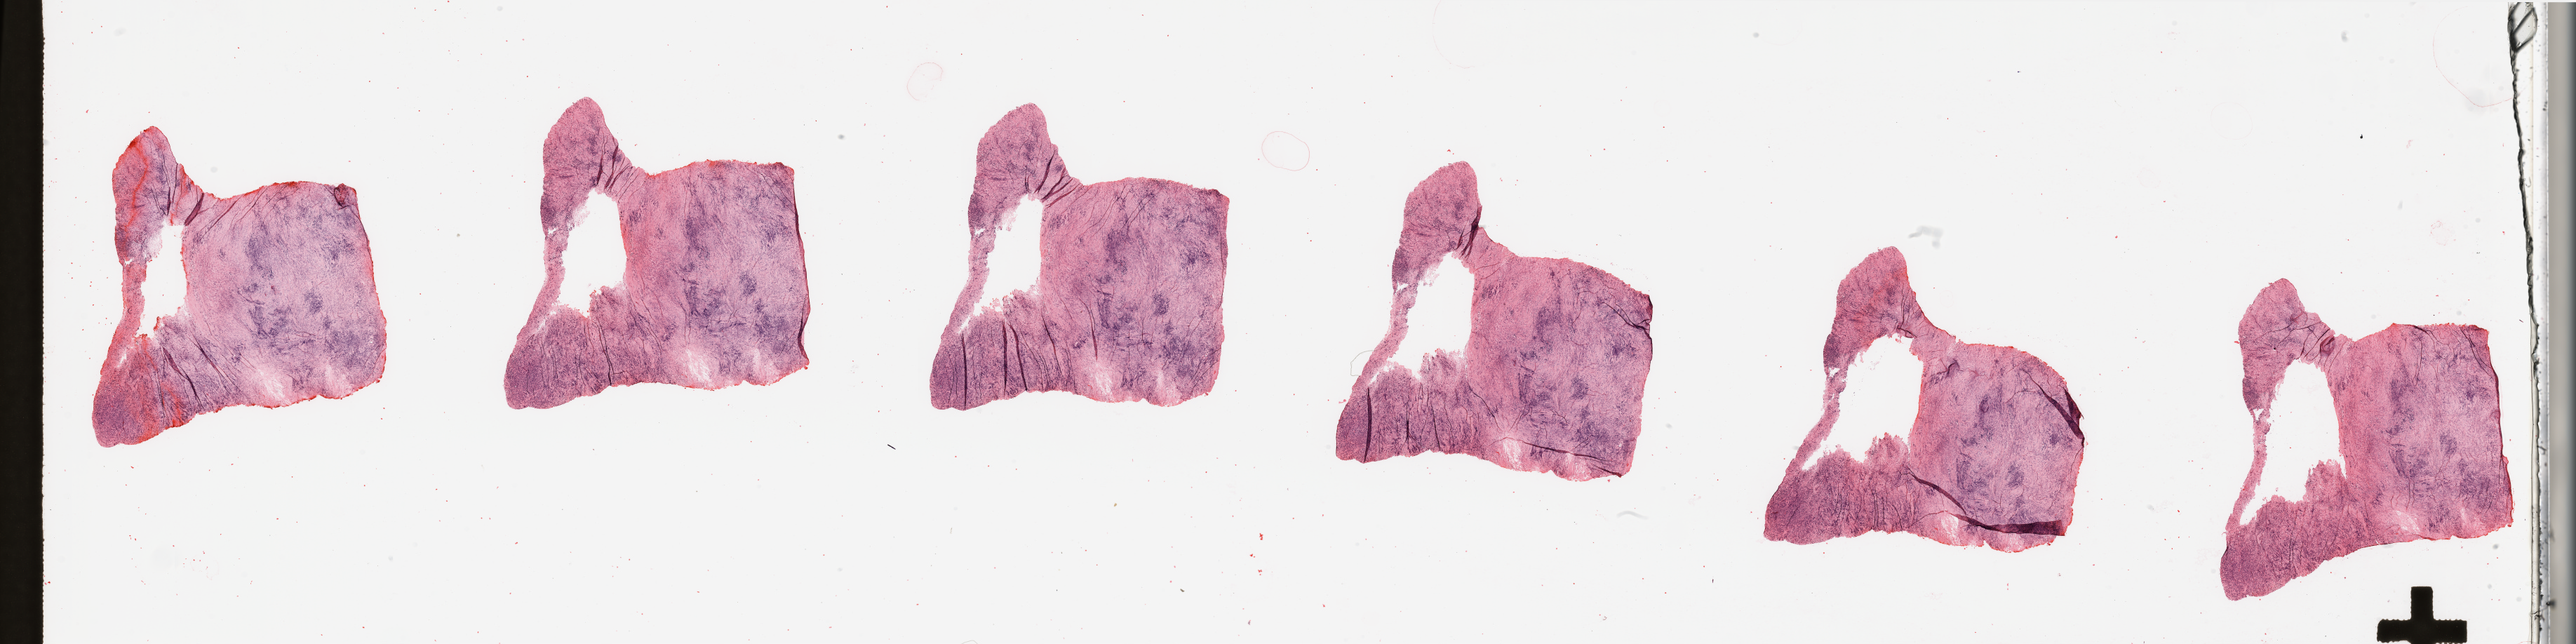
Whole-slide histology image, Hematoxylin and eosin (H&E) stained, whole scanned area (about 58.1 x 14.5 mm, slide scanned at 20x) shown as a low-resolution overview, tumour tissue sample, sampled site: lymph node. Patient: female, age 58 years.
• patient diagnosis: Malignant melanoma, NOS